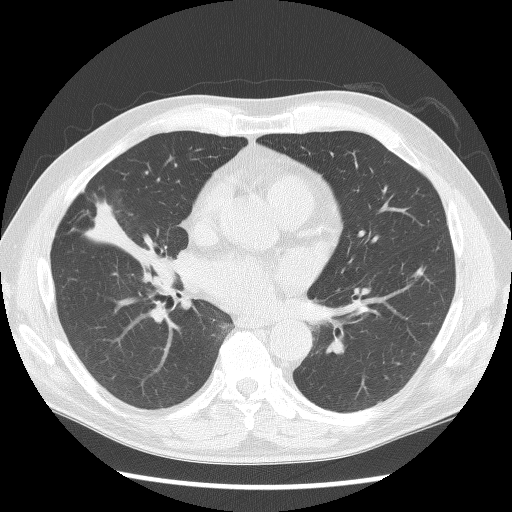
Low-dose screening chest CT, axial slice. Third annual screen. Lung window (W 1500 / L -600 HU). Lung (sharp) reconstruction kernel (BONE). 120 kVp. Slice 73 of 146 in the series. 512 × 512 image matrix, field of view 350 × 350 mm. Male participant, aged 57 years at enrolment. Former smoker at enrolment.
Expert reader's lesion annotation, bounding box (x1, y1, x2, y2) in pixels: (142, 251, 181, 292). The exam's reader record, not a measurement of the box and not confirmed to be the same lesion: non-calcified nodule or mass ≥4 mm, right middle lobe, 19 × 18 mm, smooth margins, soft tissue attenuation, pre-existing on the prior screen: yes; interval growth: yes. Lung cancer was diagnosed 69 days after this screen: carcinoid tumor, NOS, right middle lobe, carcinoid, stage not assessed, 15 mm at pathology.